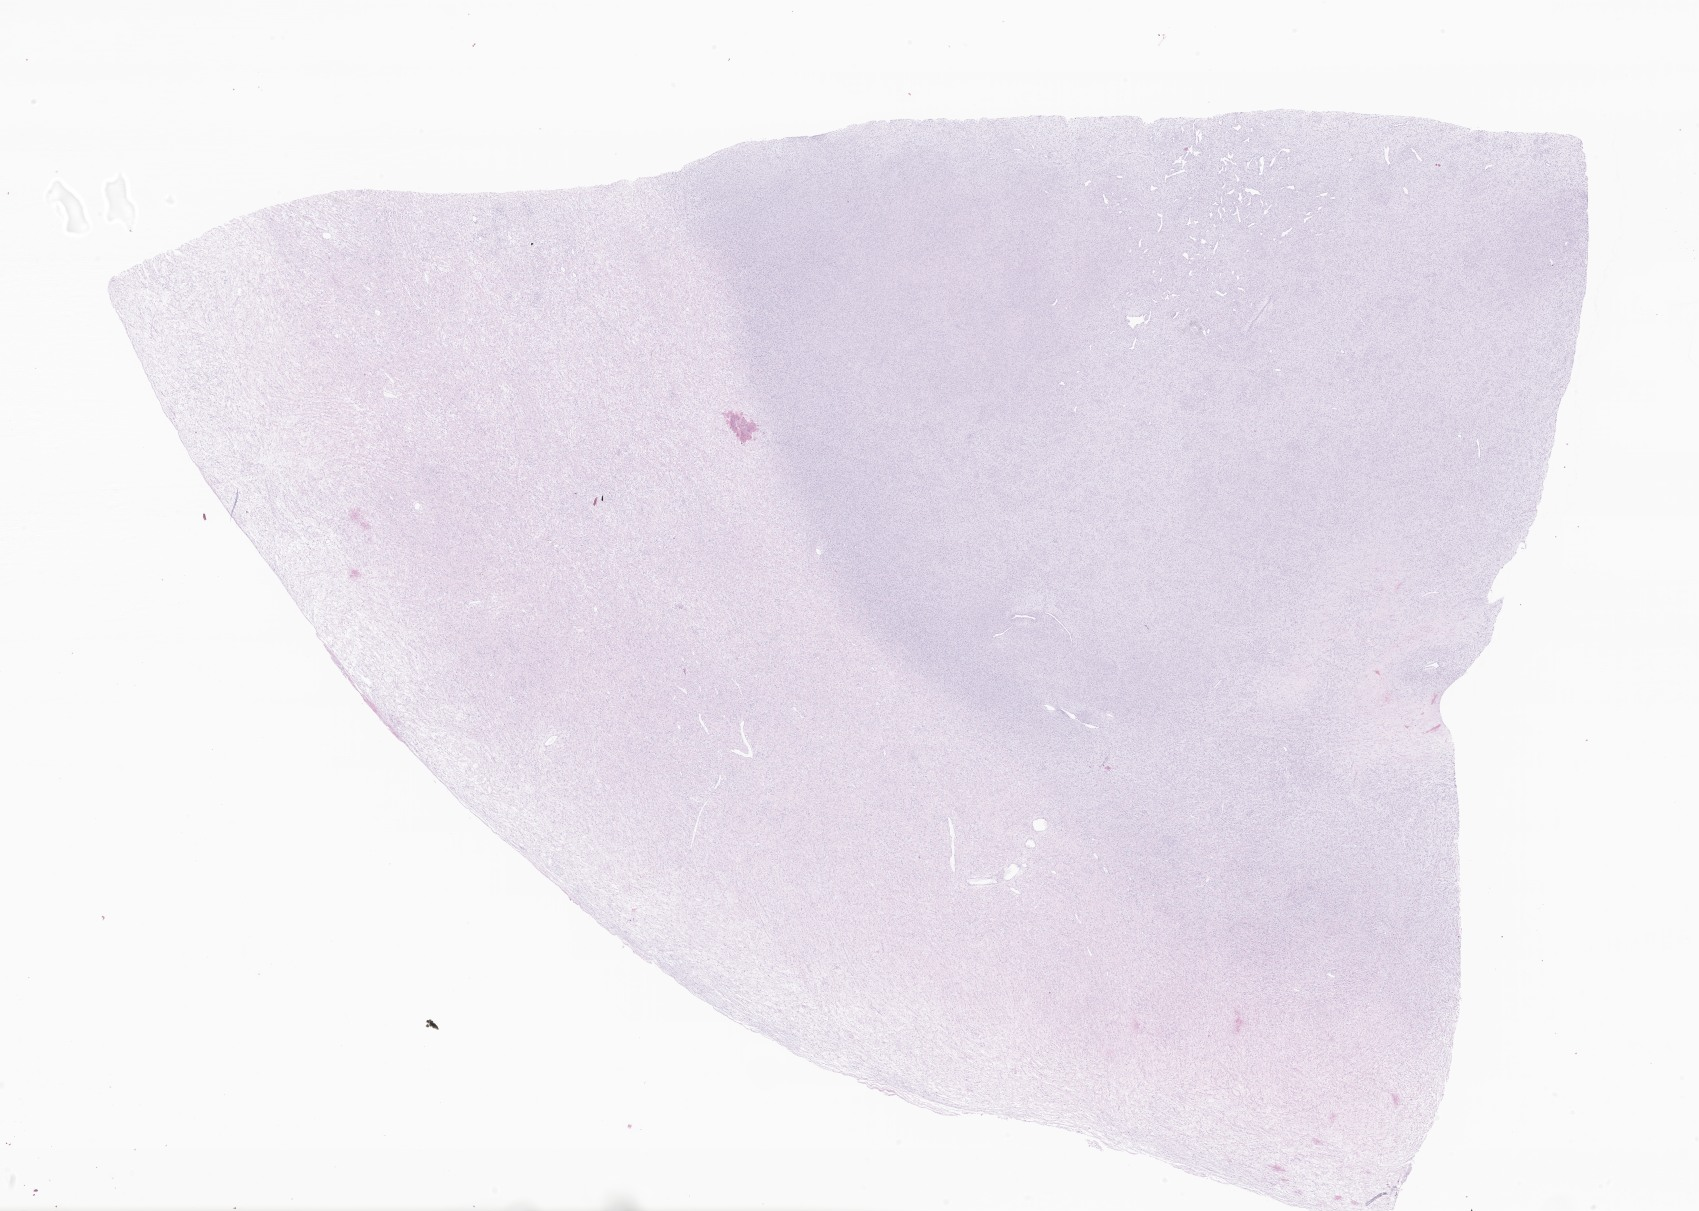
H&E whole-slide image of tumor tissue from the autonomic nervous system, a low-resolution overview of the entire scanned area, about 28.7 x 20.4 mm, formalin-fixed paraffin-embedded section. Patient female; age 117 months (9 years 9 months).
Diagnosis: Malignant peripheral nerve sheath tumor, NOS.